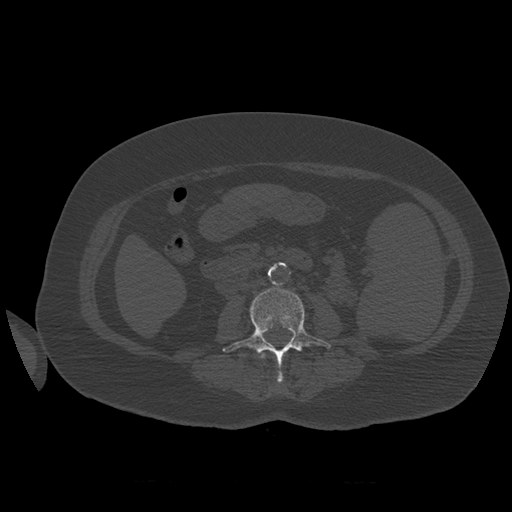
CT including the spine, one axial slice; position 231 of 399 along the scan axis; 120 kVp; bone window (W 1800 / L 400 HU); 1.25 mm slice thickness; 512 × 512 image matrix. Patient age 81 years. Case-level facts recorded for this patient, not image findings: primary cancer: renal; vertebrae with lytic lesions (as recorded): L1.
Annotated regions visible in this slice (semi-automatically segmented with operator editing):
- L2 vertebra: bounding box [x1, y1, x2, y2] px = [261, 353, 266, 359]
- L3 vertebra: [223, 287, 331, 383]